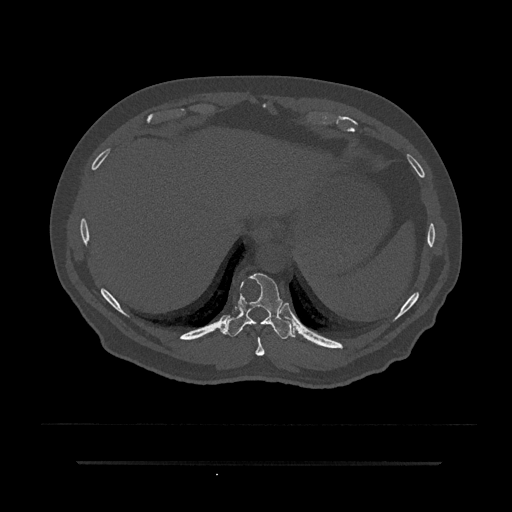
CT including the spine, one axial slice. Slice 337 of 797 in the series (ordered by position). Bone window (W 1800 / L 400 HU). 512 × 512 image matrix, field of view 464 × 464 mm. Male patient, age 59 years. Case-level facts recorded for this patient, not image findings: primary cancer: bile ducts; vertebrae with lytic lesions (as recorded): T10.
Structures marked on this image (semi-automatically segmented with operator editing):
- T10 vertebra: bounding box [x1, y1, x2, y2] px = [224, 273, 296, 339]
- T9 vertebra: [255, 337, 265, 356]